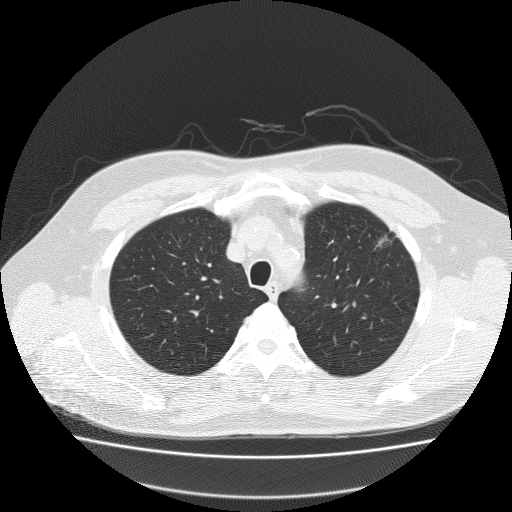
Low-dose screening chest CT, axial slice, baseline screening round, lung window (W 1500 / L -600 HU), 2 mm slice thickness, lung (sharp) reconstruction kernel (FC51). Male, age 62 years at enrolment.
Expert reader's lesion annotation, bounding box [x1, y1, x2, y2] px = [345, 220, 413, 270]. Reader record for this screening exam (exam-level; its link to the box is not recorded): non-calcified nodule or mass ≥4 mm, left upper lobe, 18 × 8 mm, spiculated (stellate) margins, soft tissue attenuation. Participant outcome: lung cancer diagnosed 49 days after this screen — bronchiolo-alveolar adenocarcinoma, NOS, left upper lobe, well differentiated (G1), stage IA (AJCC 6th edition), 25 mm at pathology.